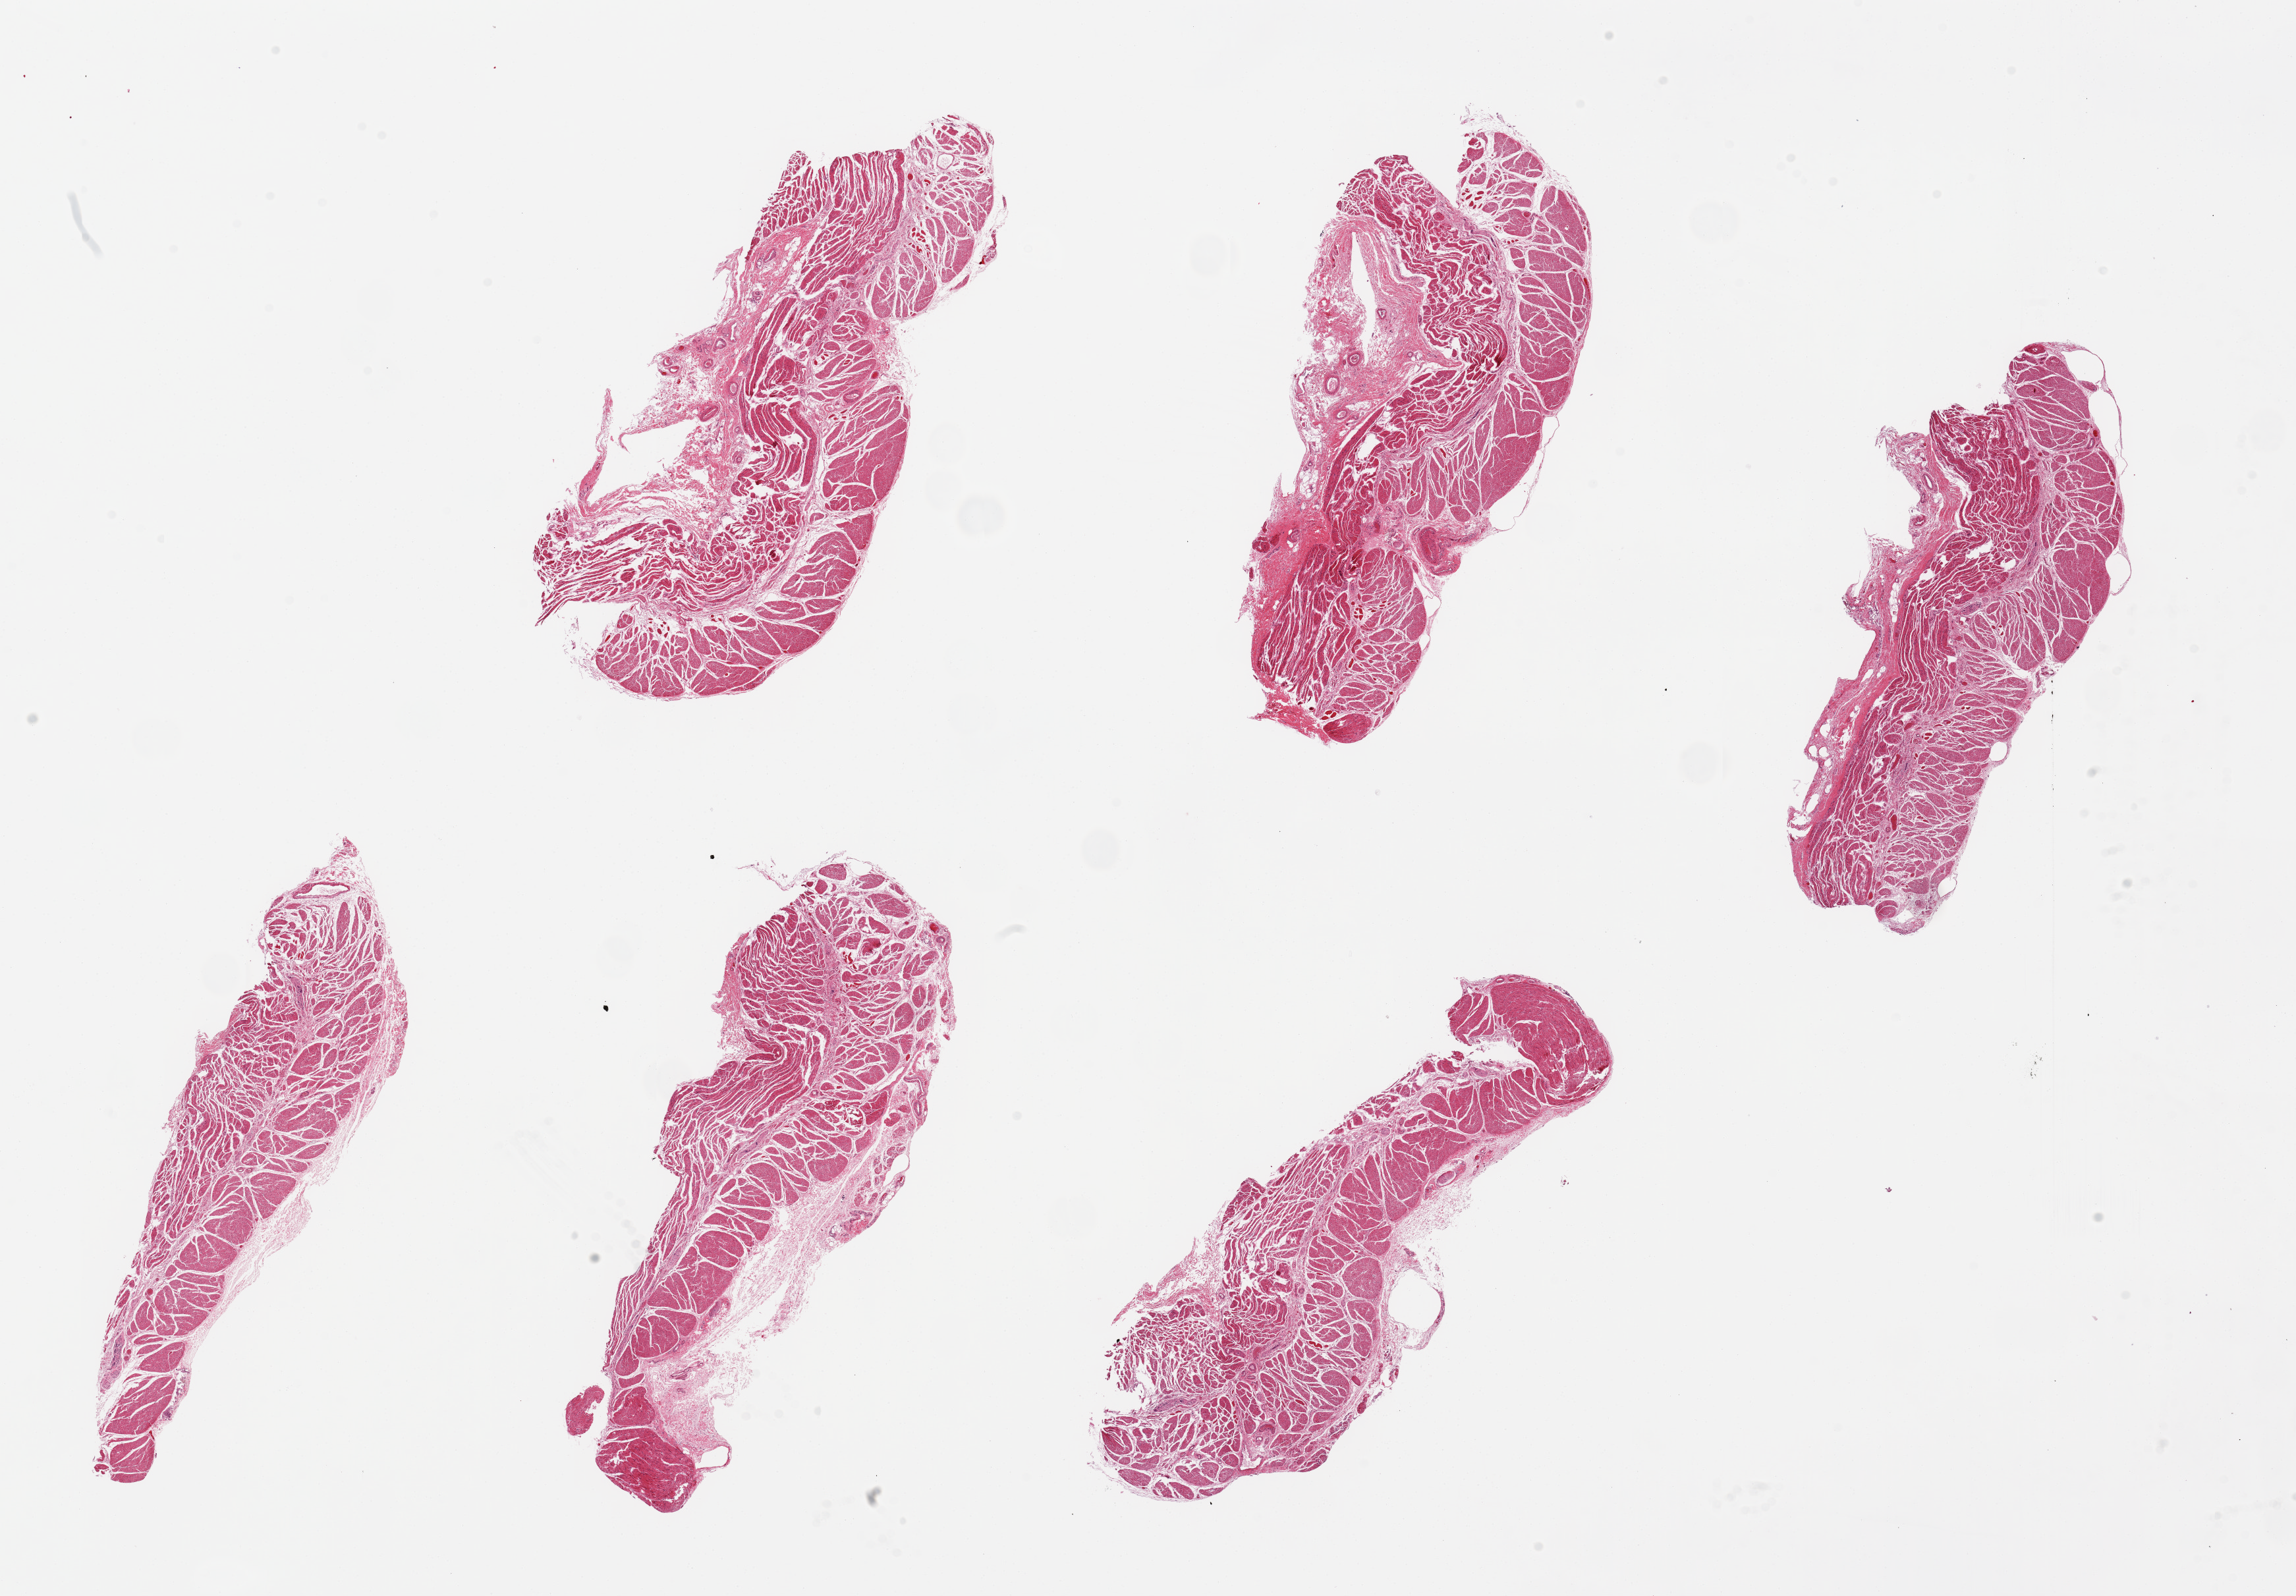
Hematoxylin and eosin (H&E) whole-slide image, brightfield, whole scanned area (about 27.6 x 19.2 mm) shown as a low-resolution overview; PAXgene-fixed, paraffin-embedded tissue; target tissue: esophageal muscle; tissue donor sample.
Review note (as recorded): 6 pieces. up to 8x4mm.